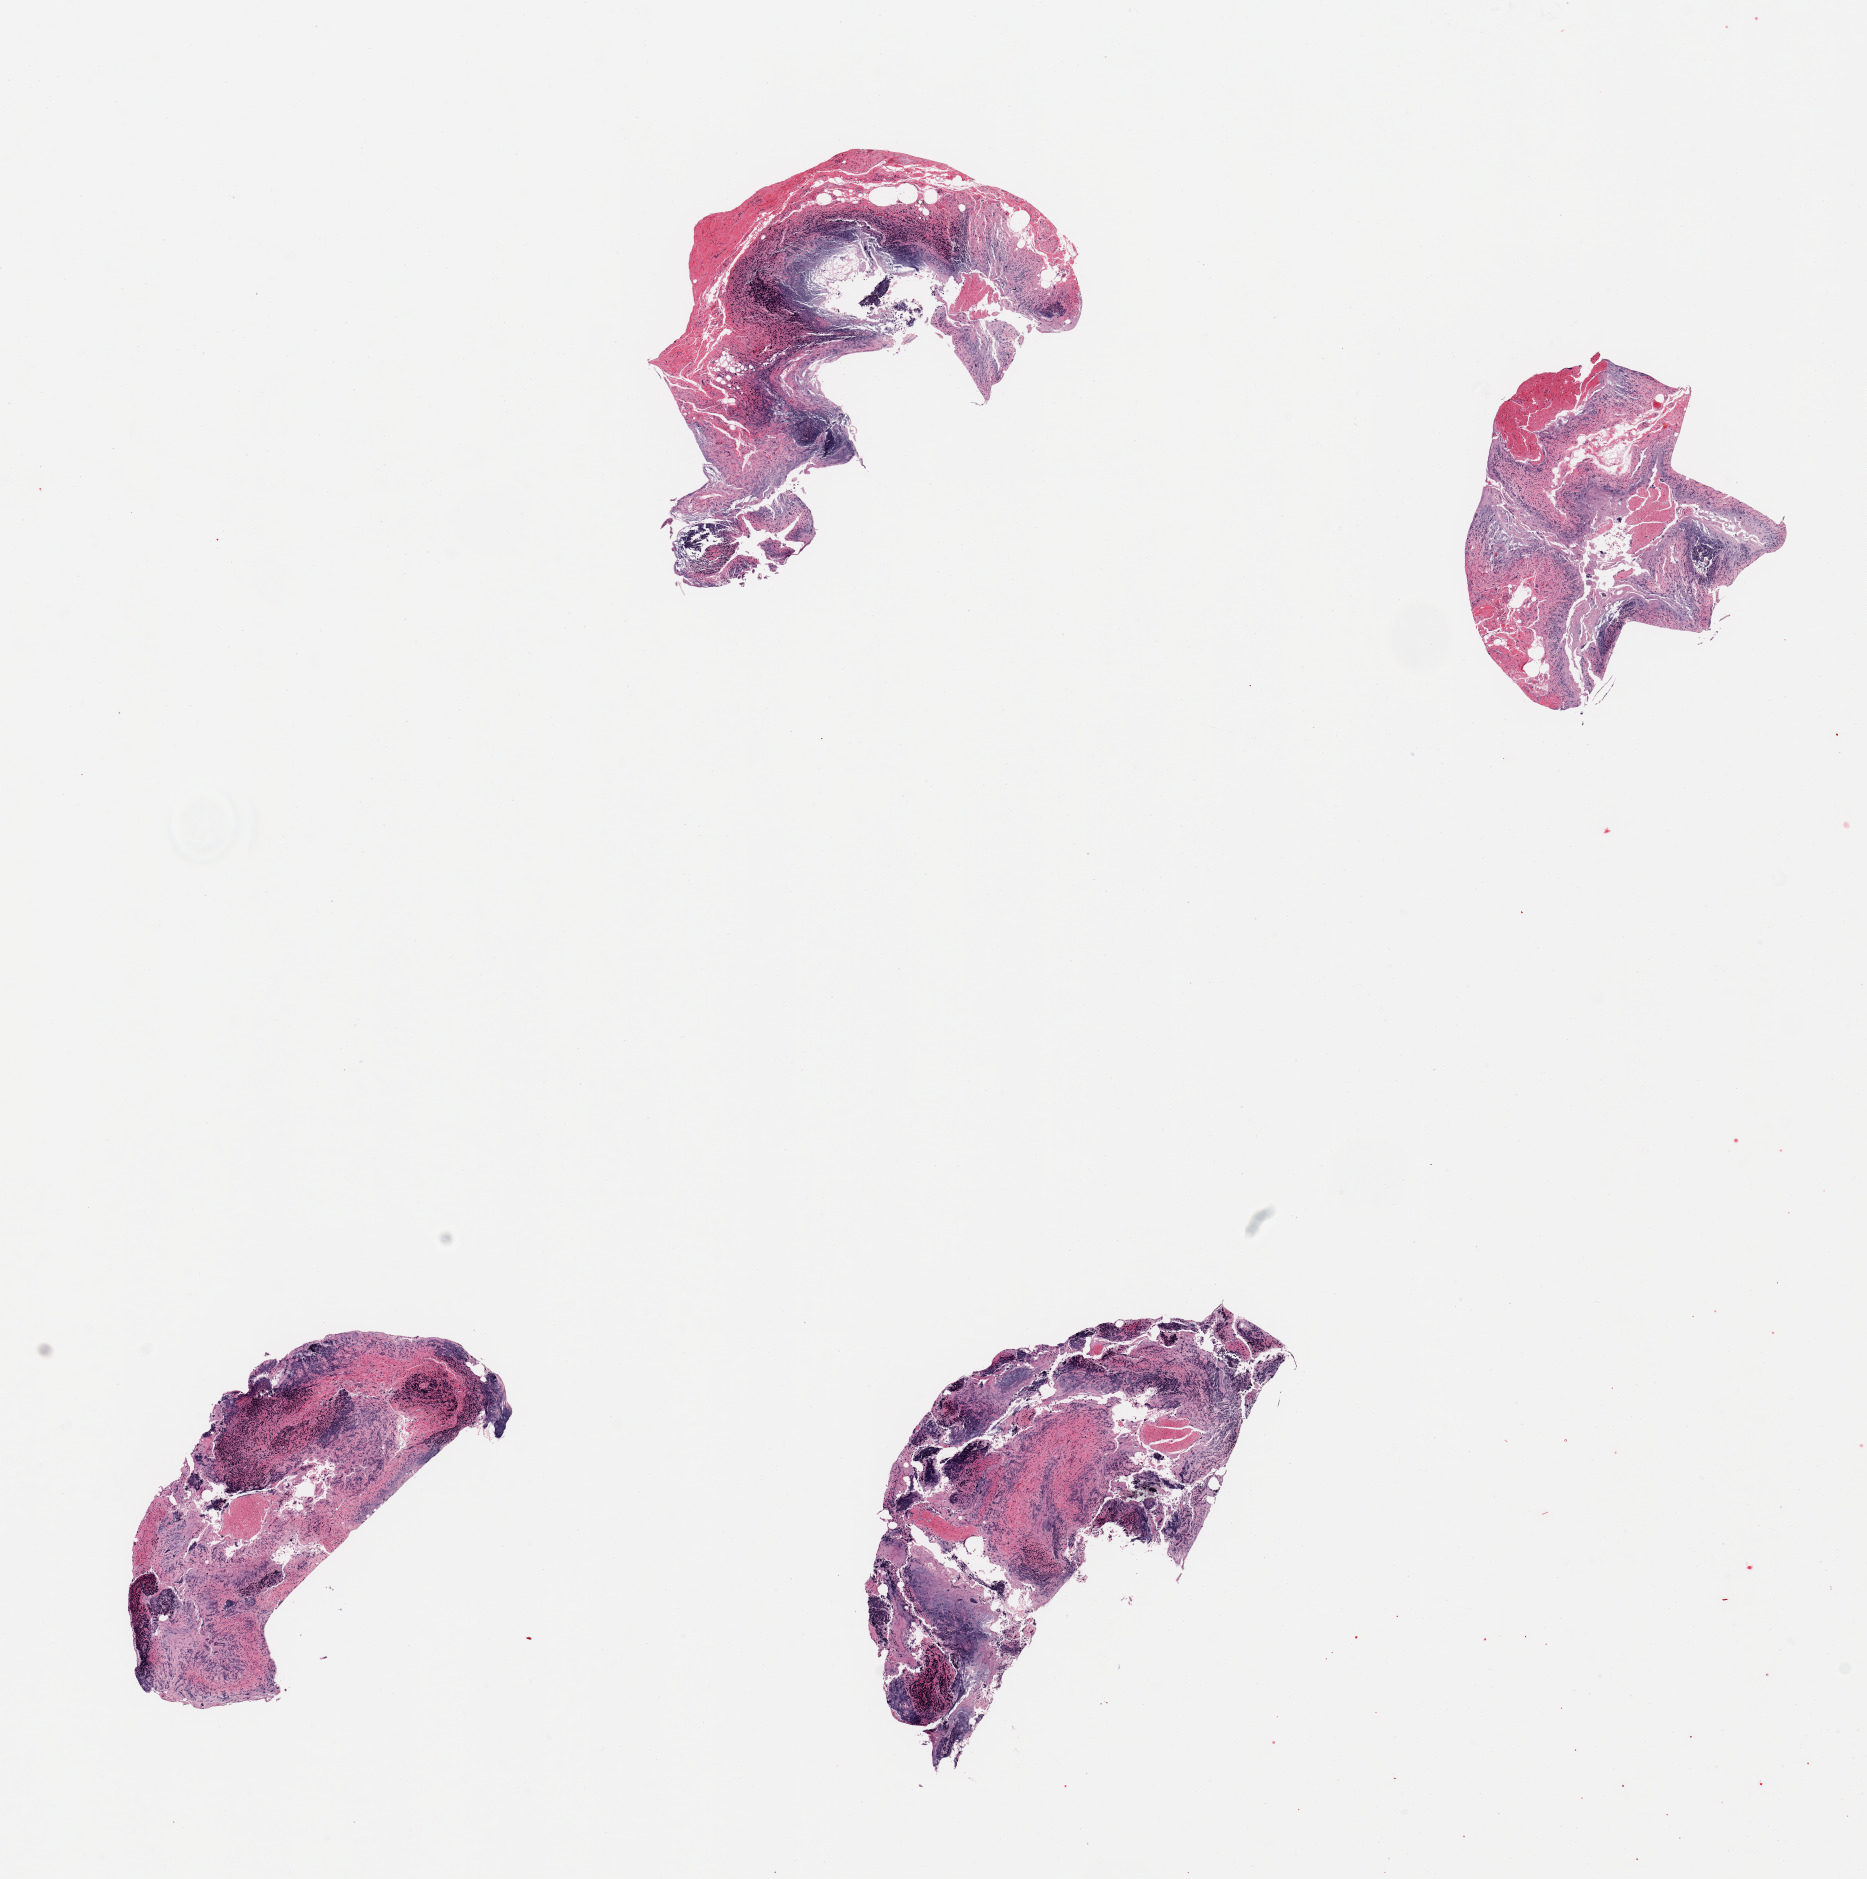
Haematoxylin and eosin whole-slide image, whole scanned area (about 14.8 x 14.9 mm) shown as a low-resolution overview; PAXgene-fixed paraffin-embedded (PFPE) section; sampled site (target tissue): ileum; donor tissue sample.
- review note (as recorded): 4 piecesm mucosa totally autolyzed; residual target lymphoid elements are ~20% total tissue